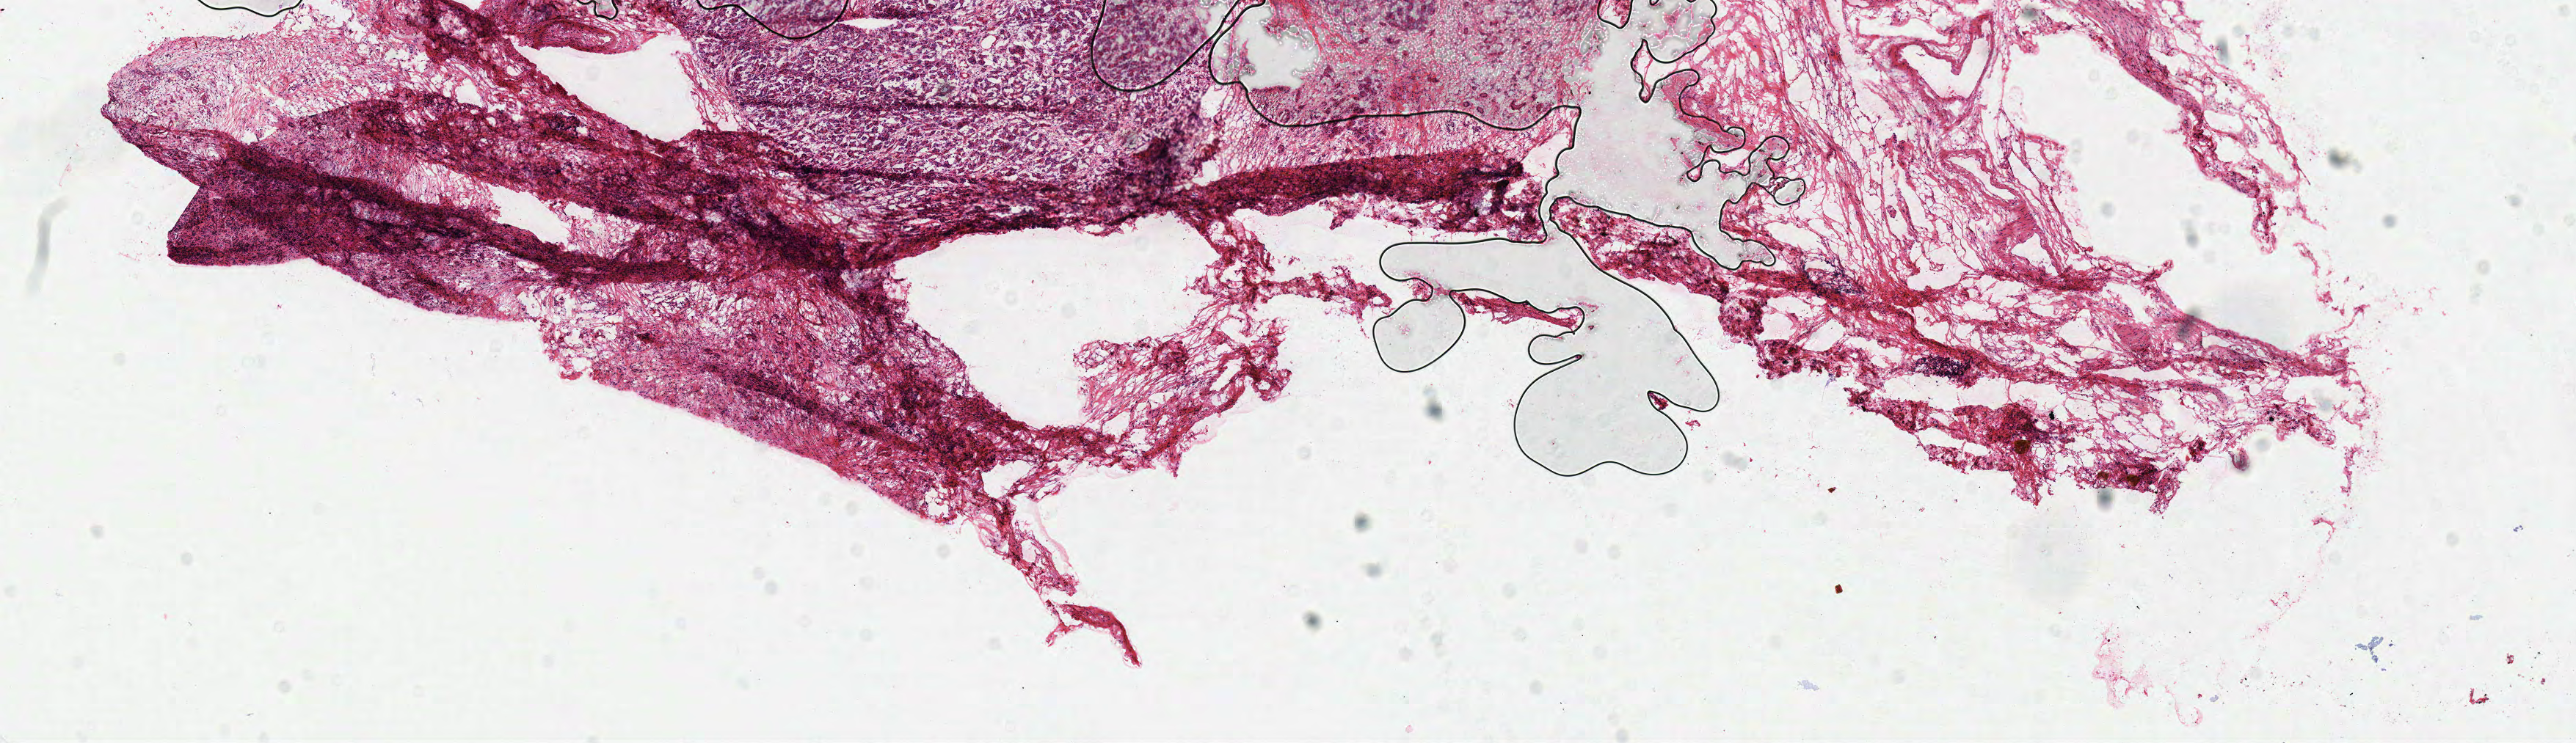
Digitized H&E tissue section (whole slide) — shown as a low-resolution overview of the whole scanned area (about 13.8 x 4.0 mm); frozen section from the top of the tissue portion; sample: solid tissue normal (non-tumour tissue), pancreas. Male, age 83 years at initial diagnosis.
This section: solid tissue normal (non-tumour) sample from the same patient. Patient diagnosis: Infiltrating duct carcinoma, NOS (head of pancreas).